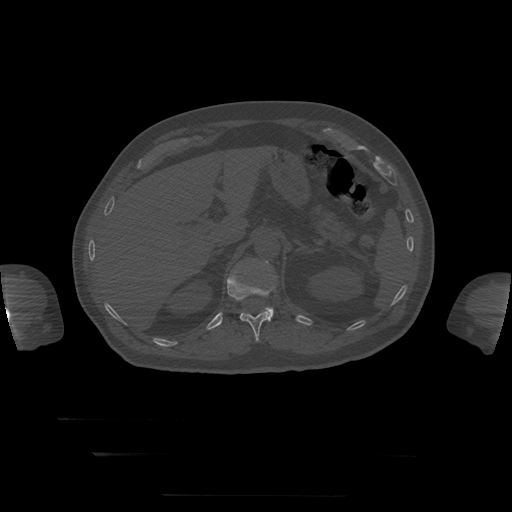
CT including the spine, one axial slice; position 67 of 397 along the scan axis; reconstruction kernel STANDARD; bone window (W 1800 / L 400 HU); 1.25 mm slice thickness; 512 × 512 image matrix, field of view 510 × 510 mm. Patient age 73 years. From the clinical record (not read from this slice): primary cancer: prostate.
Annotated regions visible in this slice (semi-automatic segmentation, software-assisted and operator-edited):
- L1 vertebra: bounding box <266,262,274,319> (left, top, right, bottom; pixels)
- T12 vertebra: <227,276,276,342>